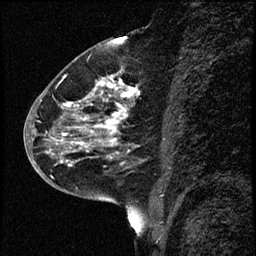
Breast MRI (dynamic contrast-enhanced), one sagittal slice; position 29 of 68 along the scan axis; dynamic contrast-enhanced study with each time point stored as its own series, time point 2 of 3 at this slice position (early post-contrast, ordered by acquisition time); 1.5 T; TE 4.2 ms, TR 17.6 ms; 2 mm slice thickness; 256 × 256 image matrix. Female patient, age 52 years. Case-level facts recorded for this patient, not image findings: setting: breast cancer imaged before/during neoadjuvant chemotherapy; receptor status: HER2-positive.
Structures marked on this image (semi-automatically segmented with operator editing):
- analysis volume of interest (the breast-tissue region the enhancement analysis was run in; not a lesion): bounding box <50,61,144,184> (left, top, right, bottom; pixels)
- tumour enhancement mask (voxels above the 100 % enhancement threshold inside the analysis volume of interest): <51,78,134,166>